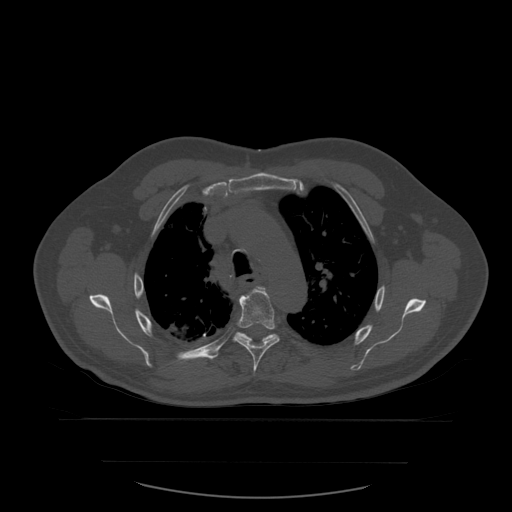
CT including the spine, one axial slice; slice 422 of 590 in the series (ordered by position); bone window (W 1800 / L 400 HU); 1.25 mm slice thickness; 512 × 512 image matrix. Patient age 71 years. From the clinical record (not read from this slice): primary cancer: lung; vertebrae with lytic lesions (as recorded): T1, T2, L5, S1.
Structures marked on this image (semi-automatic segmentation, software-assisted and operator-edited):
- T4 vertebra: bounding box (x1, y1, x2, y2) in pixels: (258, 287, 265, 290)
- T5 vertebra: (233, 287, 280, 374)
- T6 vertebra: (238, 332, 277, 342)